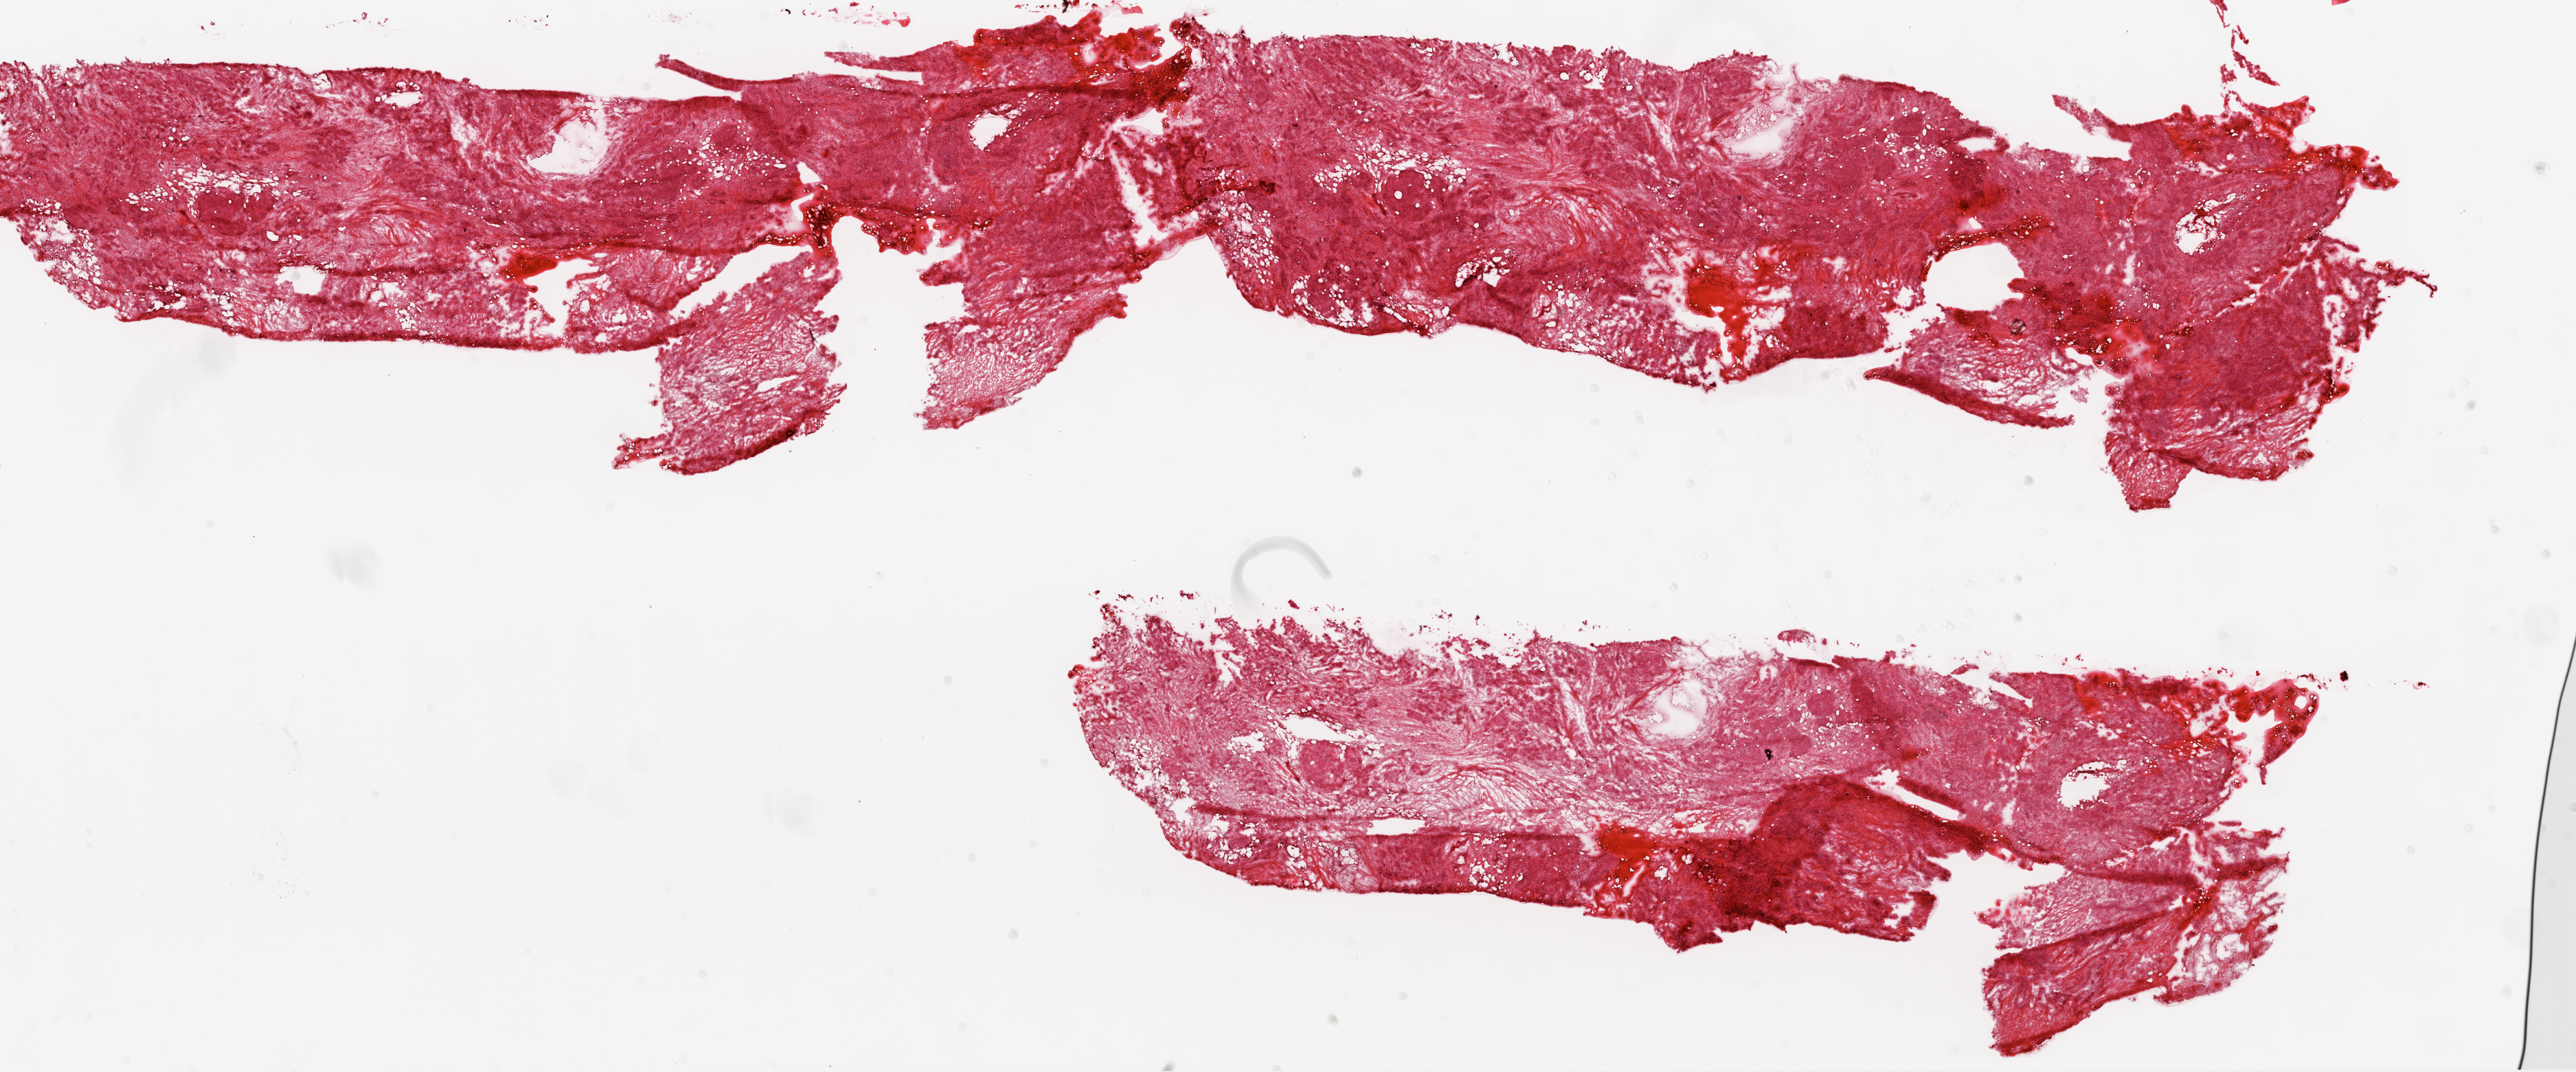
Hematoxylin and eosin (H&E) stained whole-slide image, shown as a low-resolution overview of the whole scanned area (about 30.1 x 12.5 mm); frozen section from the top of the tissue portion; ovary, primary tumour sample. Patient: female, age at initial diagnosis 46 years. Slide review estimates, as recorded: tumour cells 60%, tumour nuclei 70%.
Pathologic diagnosis: Serous cystadenocarcinoma, NOS.